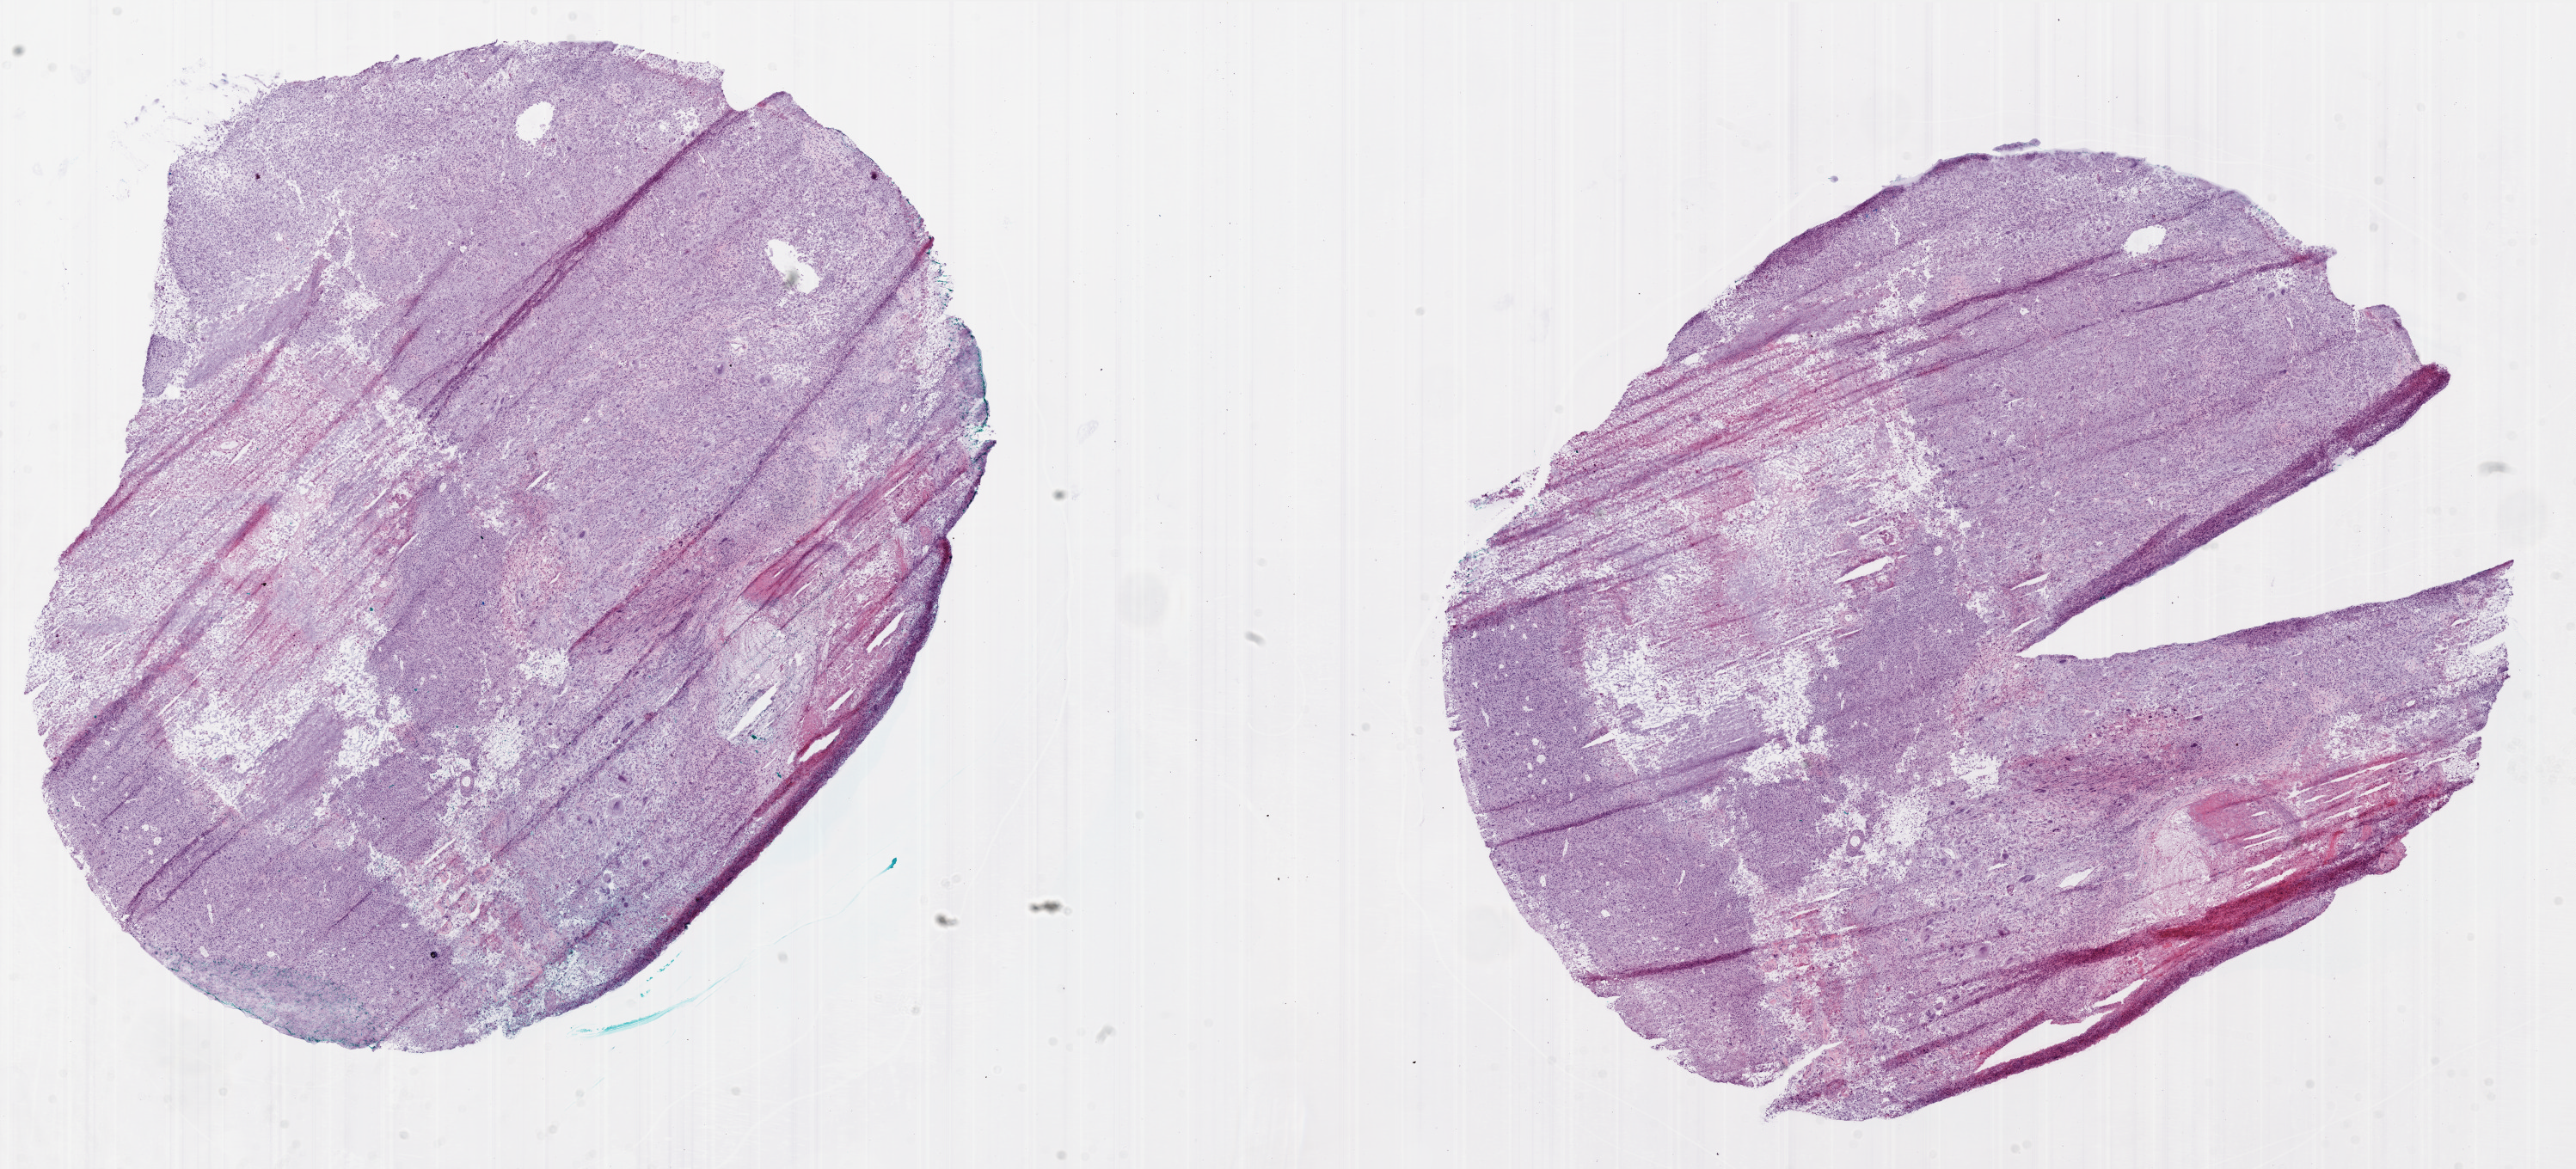
Digitized Hematoxylin and eosin (H&E) stained tissue section (whole slide) — whole scanned area (about 24.0 x 10.9 mm, slide scanned at 20x) shown as a low-resolution overview, frozen section, sample: primary tumour, brain. Patient: male, age at initial diagnosis 34 years. Pathologist review of this section (percent, as recorded): tumour cells 75%, tumour nuclei 90%, normal cells 0%, stromal cells 0%, necrosis 25%.
- histologic diagnosis: Glioblastoma